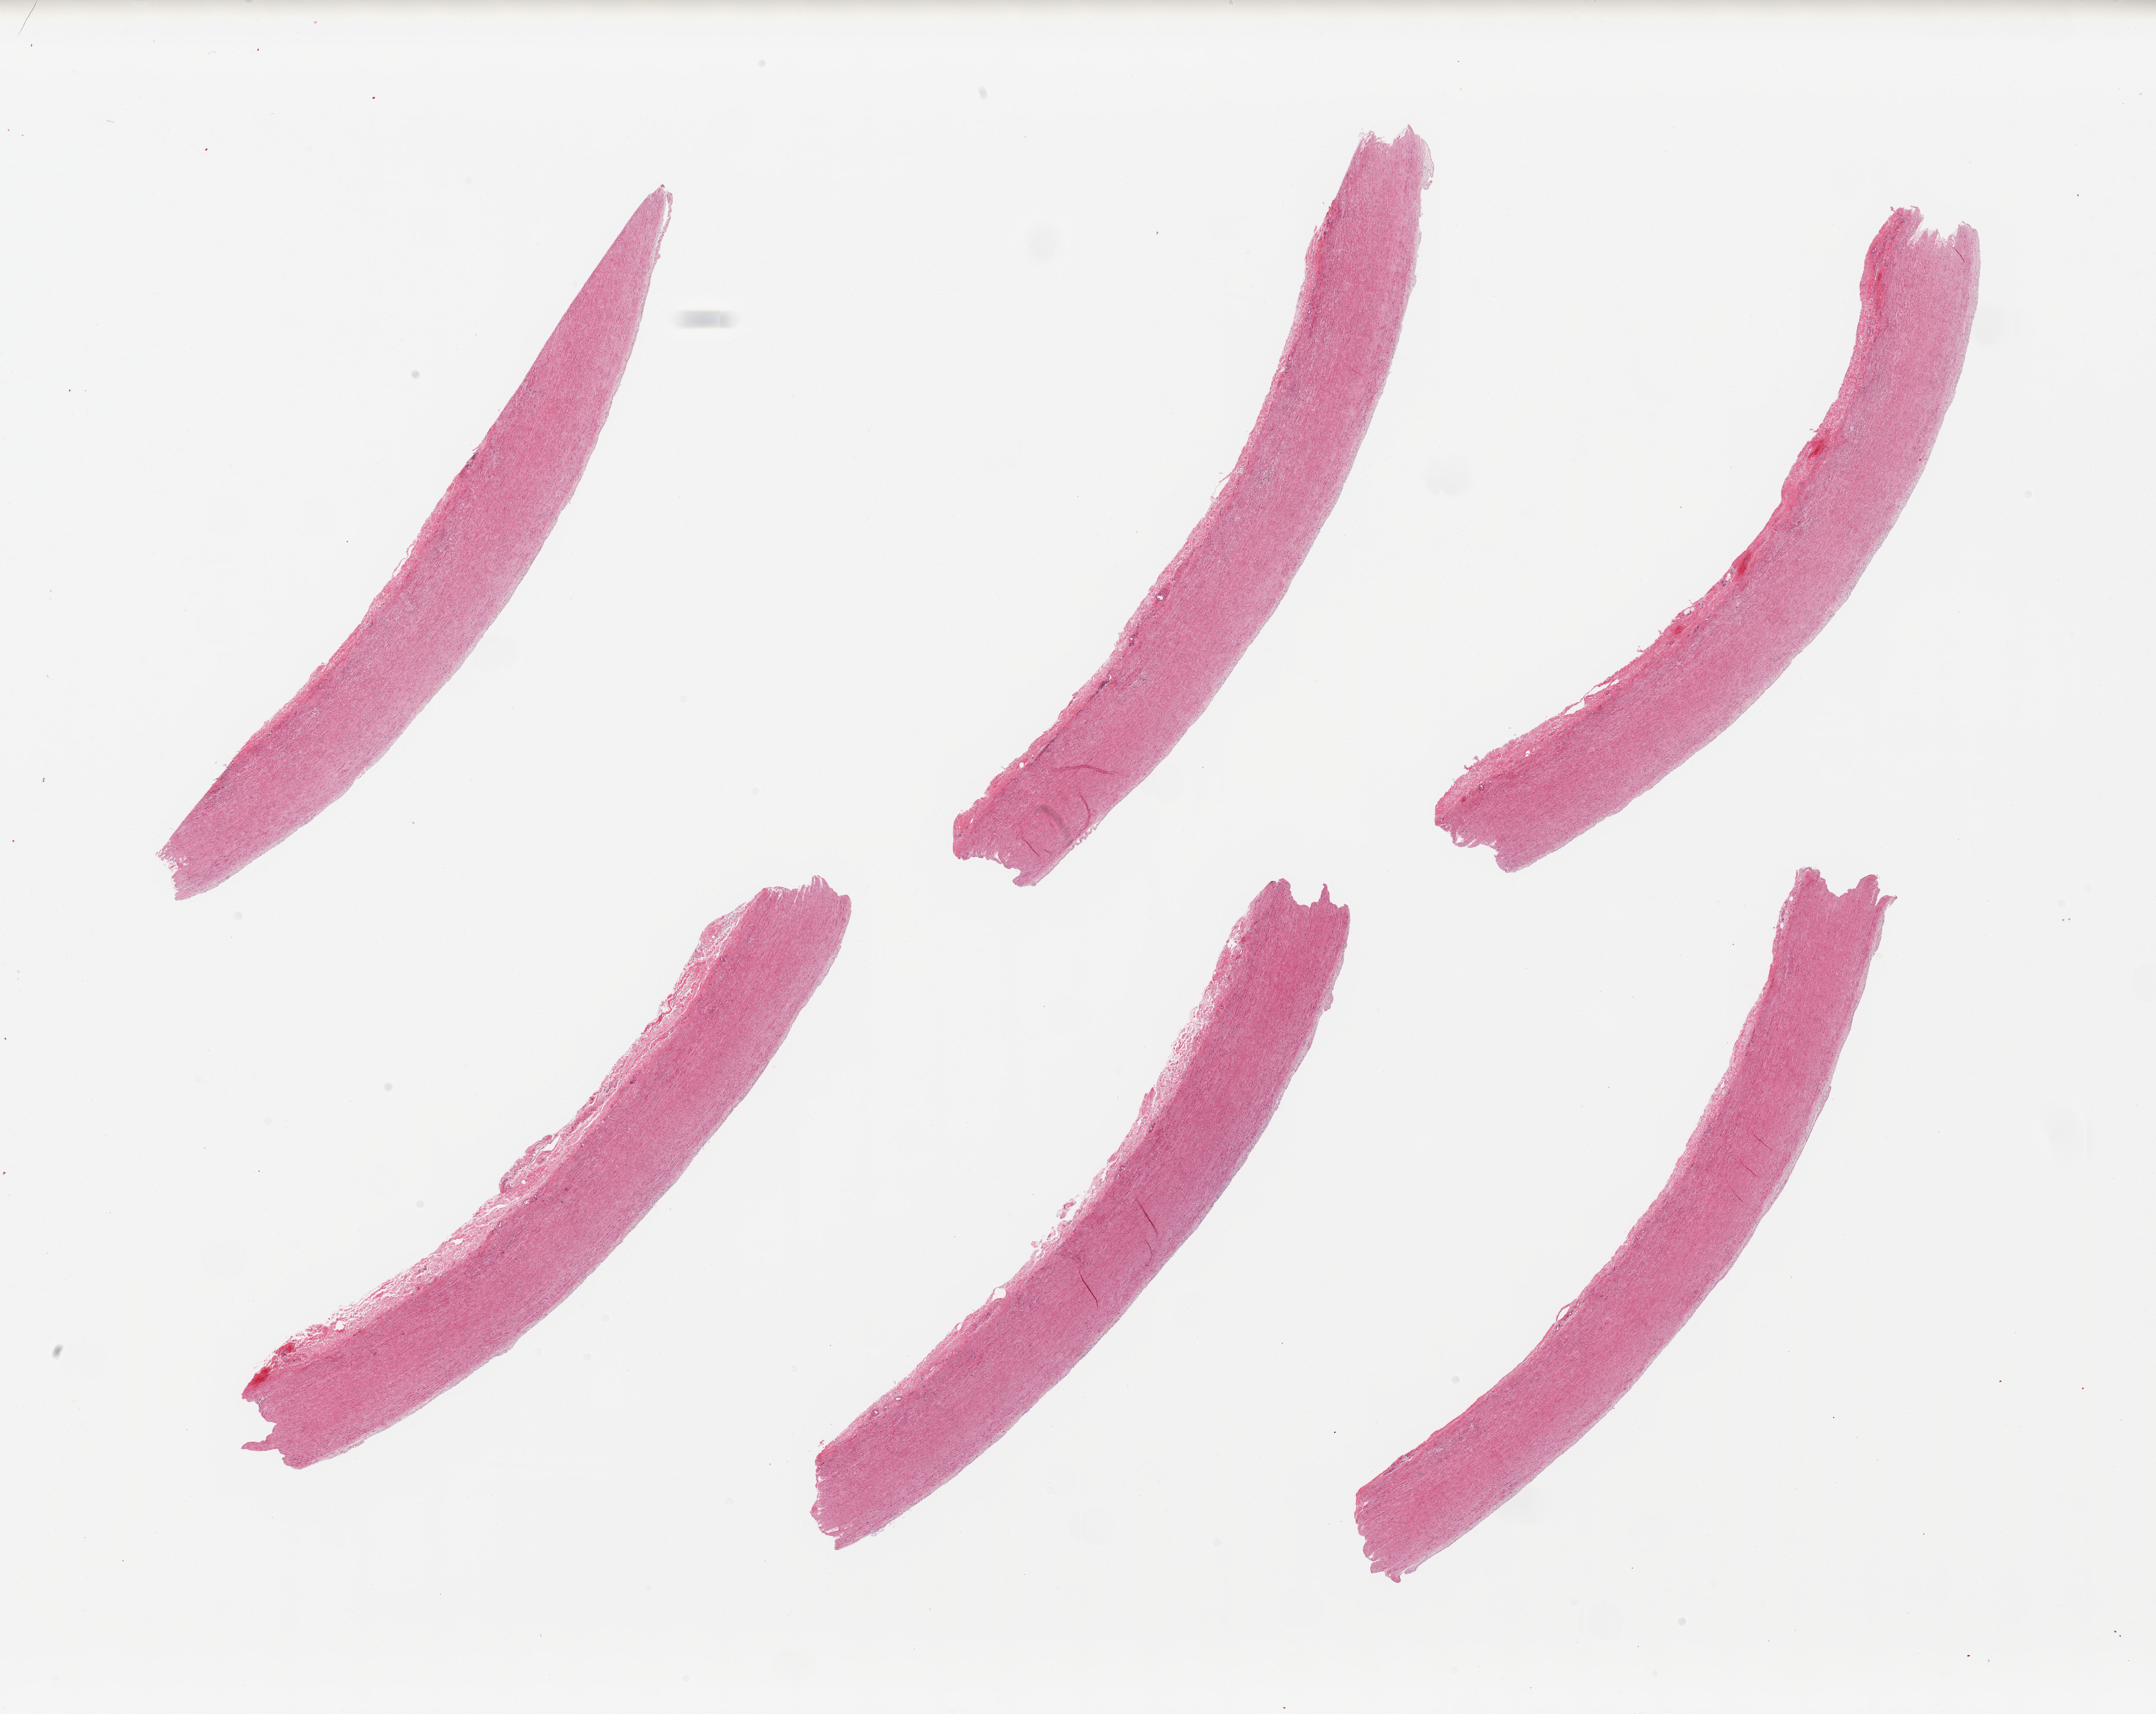
Hematoxylin and eosin (H&E) whole-slide image, whole scanned area (about 29.5 x 23.5 mm) shown as a low-resolution overview. PAXgene-fixed paraffin-embedded (PFPE) section. Target tissue: aorta. Tissue donor sample. Donor sex: female.
- reviewer comment on this tissue sample: 6 pieces, minimal atherosis